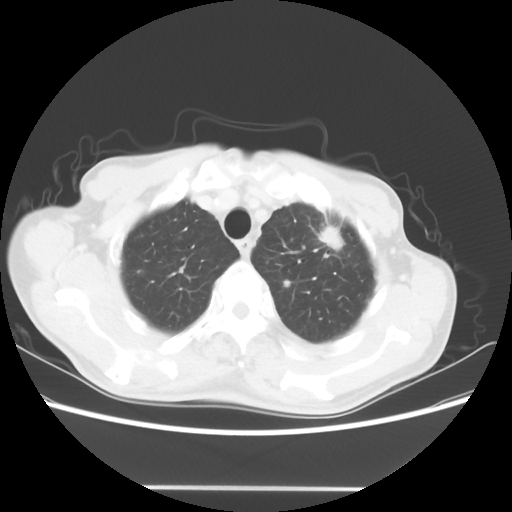
Chest CT, one axial slice. Slice 50 of 60 in the series (ordered by position). 100 kVp. Lung window (W 1500 / L -600 HU). 512 × 512 image matrix, field of view 367 × 367 mm. Male patient, age 74 years. From the clinical record (not read from this slice): clinical TNM (as recorded): T1c N0 M1a.
Outlined on this slice (bounding box drawn by a radiologist):
- lung tumour (recorded histology: adenocarcinoma): bounding box [x1, y1, x2, y2] px = [321, 228, 340, 245]